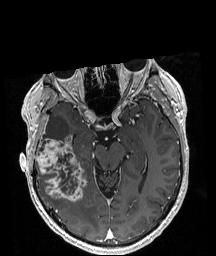
Brain MRI from a brain-tumour surgery series, one axial slice. Slice 122 of 208 in the series (ordered by position). T1-weighted post-contrast. 1 mm slice thickness. 216 × 256 image matrix, field of view 211 × 250 mm. Case-level facts recorded for this patient, not image findings: histopathology: Astrocytoma; WHO grade: 4; IDH mutation: yes; tumour location: Right Temporal.
Outlined on this slice (outlined manually by an expert reader):
- tumour: bounding box <35,134,87,202> (left, top, right, bottom; pixels)